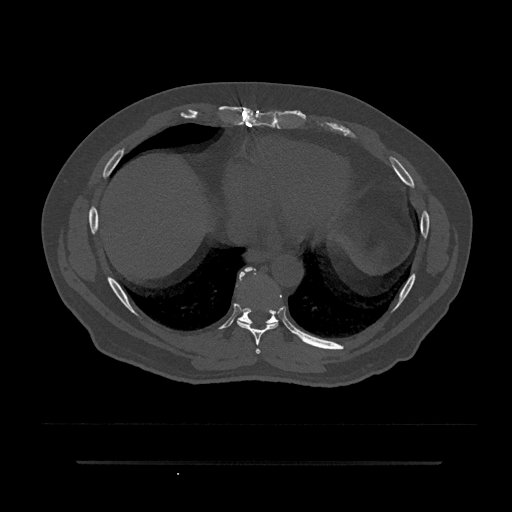
CT including the spine, one axial slice. Slice 407 of 797 in the series (ordered by position). 120 kVp. Bone window (W 1800 / L 400 HU). 512 × 512 image matrix, field of view 464 × 464 mm. Male patient, age 59 years. Case-level facts recorded for this patient, not image findings: primary cancer: bile ducts.
Annotated regions visible in this slice (semi-automatic segmentation, software-assisted and operator-edited):
- T7 vertebra: box from (x=255, y=348) to (x=260, y=354) px
- T8 vertebra: (x=237, y=267)–(x=278, y=345)
- T9 vertebra: (x=237, y=267)–(x=280, y=327)